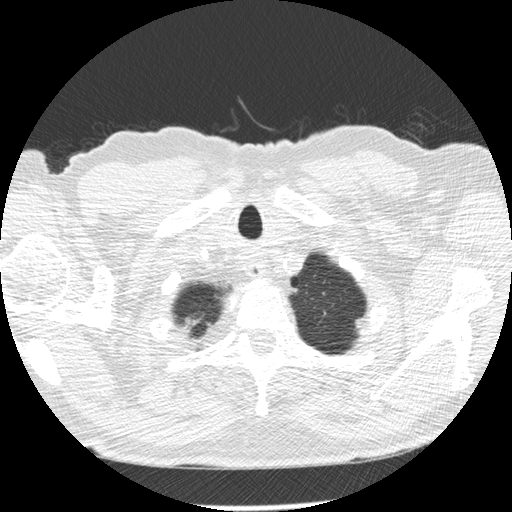
Chest CT (low-dose screening protocol), one axial image; second screening round (one year after baseline); lung window (W 1500 / L -600 HU); 2.5 mm slice thickness; slice 19 of 276 in the series; 512 × 512 image matrix. Male participant, aged 73 years at enrolment. Former smoker at enrolment.
Expert-annotated lung lesion, bounding box [x1, y1, x2, y2] px = [342, 307, 382, 345]. Screening reader's record for this exam: no non-calcified nodule ≥4 mm recorded. Official screen result: negative screen, minor abnormalities not suspicious for lung cancer. Lung cancer was diagnosed 457 days after this screen (after the third annual screen): adenocarcinoma, NOS, left upper lobe, poorly differentiated (G3), stage IB (AJCC 6th edition), 10 mm at pathology.